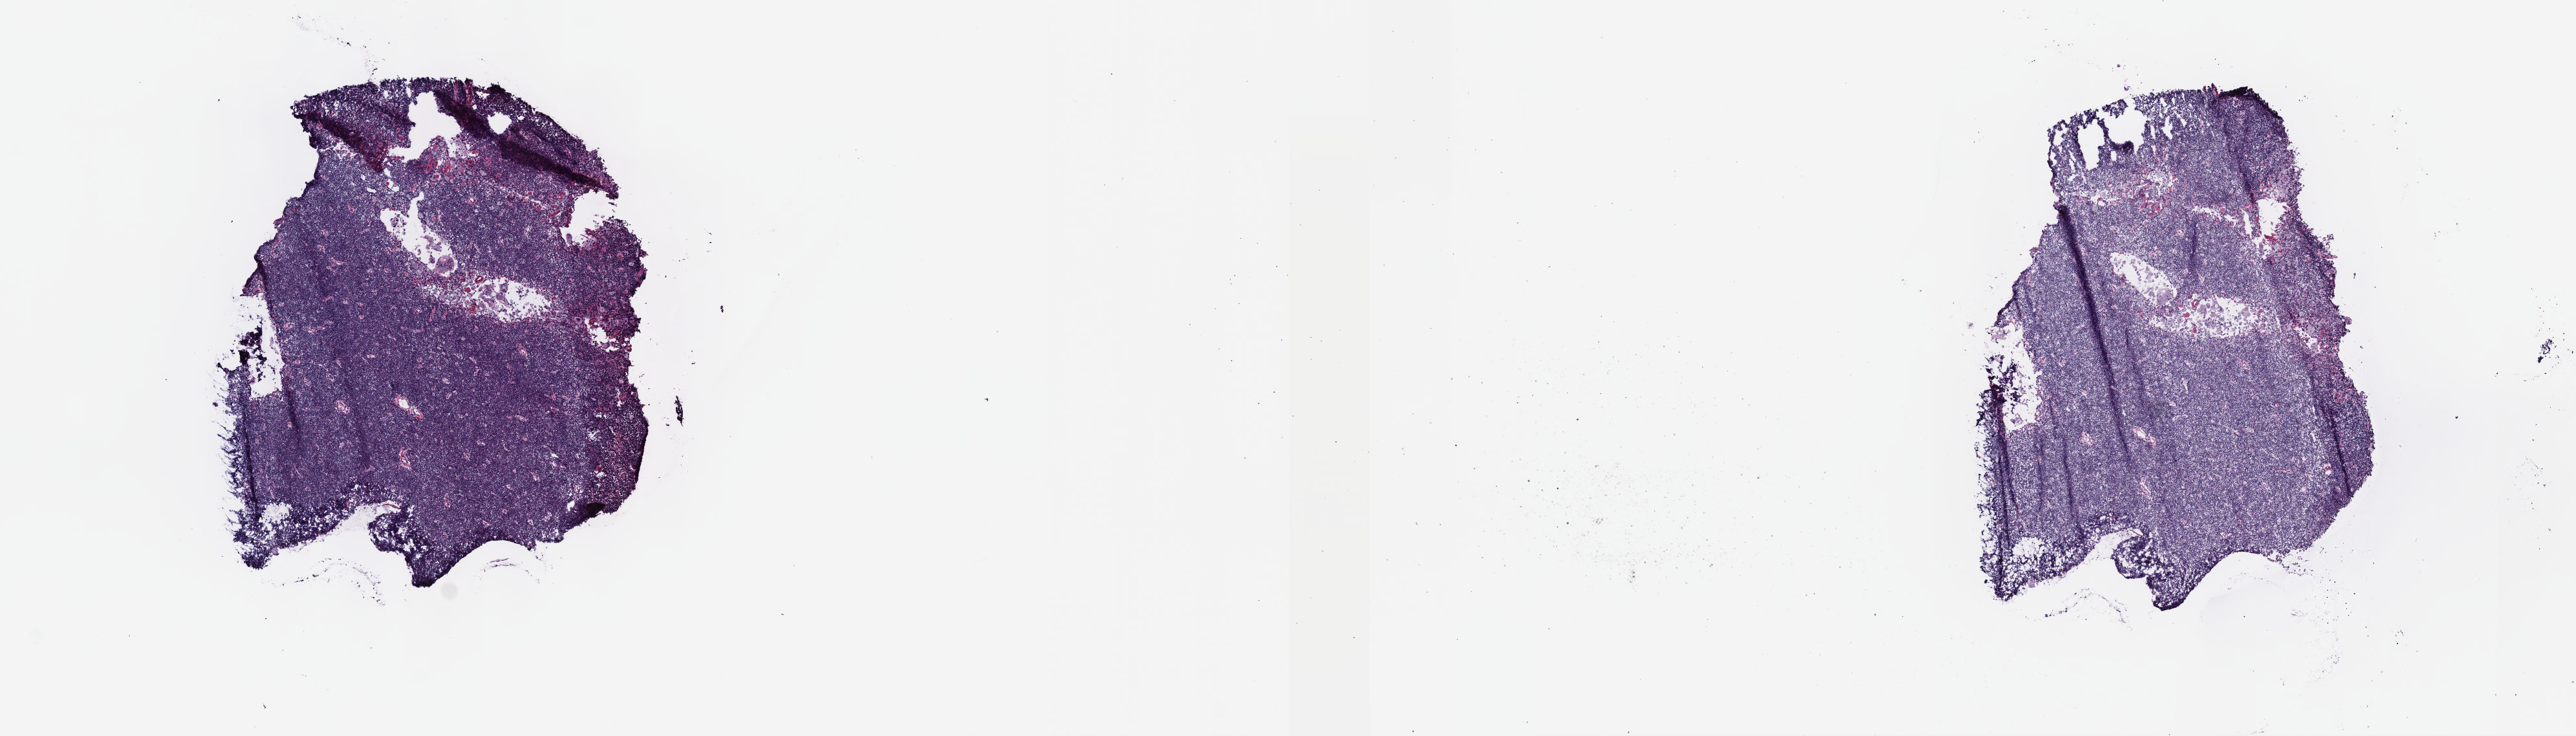
Hematoxylin and eosin (H&E) stained whole-slide image — whole scanned area (about 16.1 x 4.6 mm, acquisition: 40x scan) shown as a low-resolution overview; frozen section from the top of the tissue portion; primary tumour sample from the thymus. Patient: male, age at initial diagnosis 37 years. Slide review estimates, as recorded: tumour cells 100%, tumour nuclei 80%, normal cells 0%, stromal cells 0%, necrosis 0%. Infiltration values recorded for this section: lymphocyte infiltration 2%, monocyte infiltration 2%, neutrophil infiltration 0%.
Diagnosis: Thymoma, type B2, malignant.